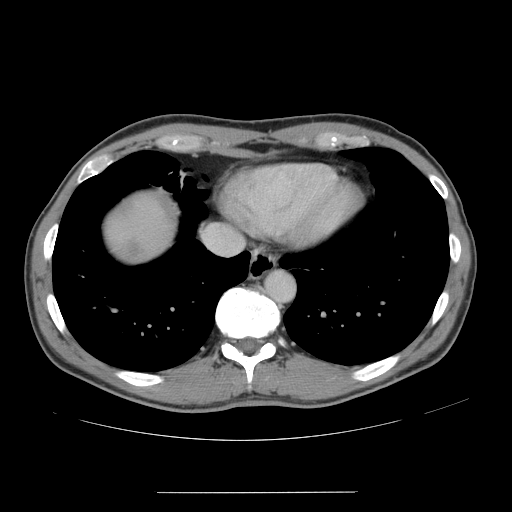
Contrast-enhanced abdominal CT, one axial slice; position 143 of 178 along the scan axis; intravenous contrast given; soft-tissue window (W 400 / L 40 HU); 2.5 mm slice thickness; 512 × 512 image matrix, field of view 401 × 401 mm. Male patient, age 53 years. From the clinical record (not read from this slice): diagnosis: colorectal cancer liver metastases, imaged before liver resection; multiple liver metastases: yes; largest metastasis: 2.4 cm.
Outlined on this slice (manually delineated by an expert):
- liver: bounding box <106,195,171,262> (left, top, right, bottom; pixels)
- liver metastasis: <127,240,140,256>